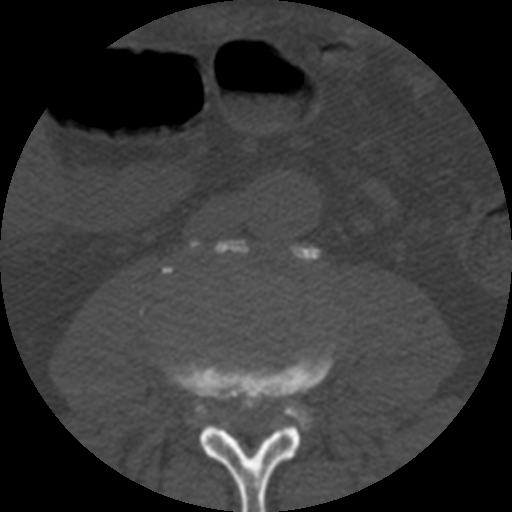
CT including the spine, one axial slice; slice 110 of 508 in the series (ordered by position); bone window (W 1800 / L 400 HU); 1.25 mm slice thickness; 512 × 512 image matrix, field of view 160 × 160 mm. Patient age 57 years. Case-level facts recorded for this patient, not image findings: primary cancer: prostate.
Outlined on this slice (semi-automatic segmentation, software-assisted and operator-edited):
- L3 vertebra: bounding box [x1, y1, x2, y2] px = [161, 343, 335, 512]
- L4 vertebra: [190, 239, 321, 429]